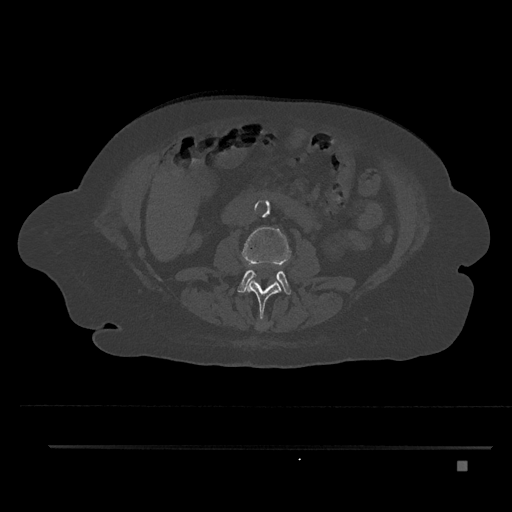
CT including the spine, one axial slice; slice 153 of 797 in the series (ordered by position); 120 kVp; bone window (W 1800 / L 400 HU); 512 × 512 image matrix. Female patient, age 76 years. Case-level facts recorded for this patient, not image findings: primary cancer: lung; vertebrae with lytic lesions (as recorded): T11, L3.
Annotated regions visible in this slice (semi-automatic segmentation, software-assisted and operator-edited):
- L2 vertebra: bounding box [x1, y1, x2, y2] px = [245, 280, 281, 329]
- L3 vertebra: [237, 227, 292, 294]